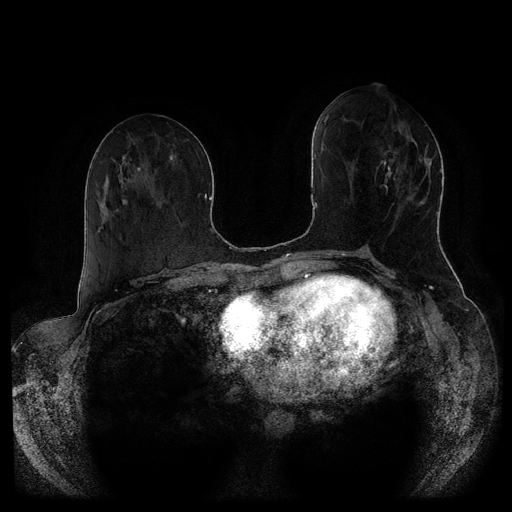
Breast MRI (dynamic contrast-enhanced, multi-phase), one axial slice. Slice 44 of 116 in the series (ordered by position). Dynamic contrast-enhanced series, time point 2 of 5 at this slice position (early post-contrast). 1.5 T. TE 2.6 ms, TR 5.3 ms. 2 mm slice thickness. 512 × 512 image matrix, field of view 370 × 370 mm. Patient: female, 51 years.
Annotated regions visible in this slice (semi-automatically segmented with operator editing):
- breast lesion (labelled 'tumour' in the annotation; benign lesions carry a separate 'benign' label): bounding box [x1, y1, x2, y2] px = [375, 146, 405, 205]